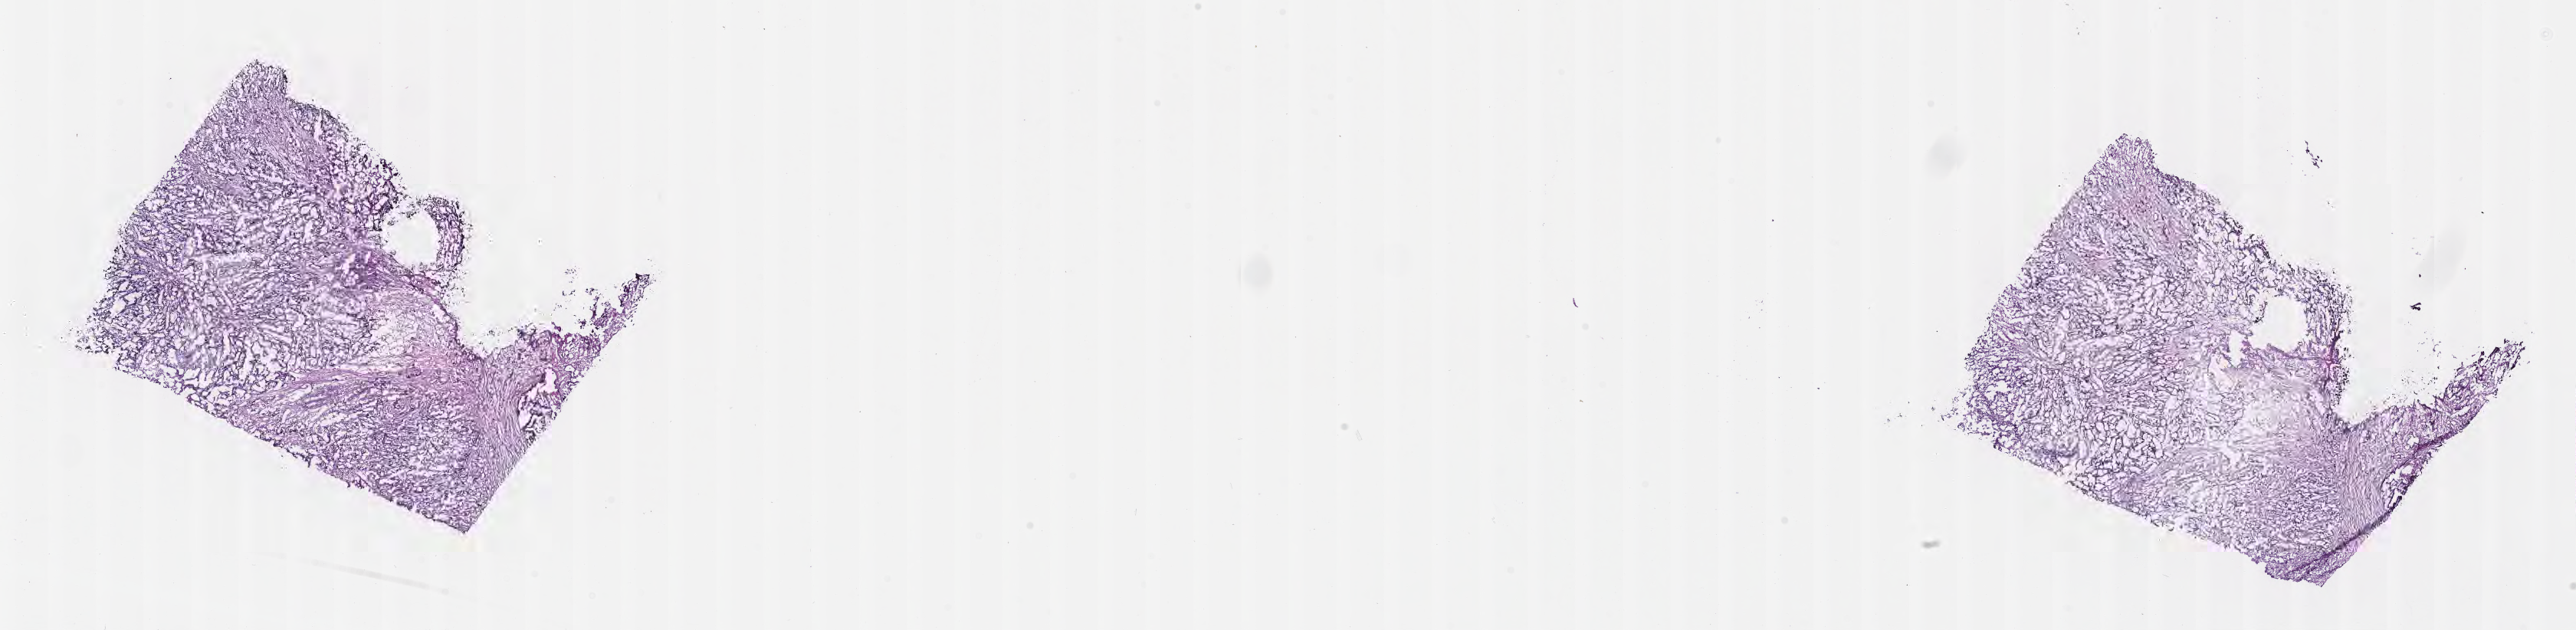
Hematoxylin and eosin (H&E) whole-slide image, shown as a low-resolution overview of the whole scanned area (about 27.2 x 6.6 mm). Frozen section. Metastatic tumor tissue, resected from liver. Female patient; age at initial diagnosis 78 years. Pathologist review of this section (percent, as recorded): tumor cells 50%, tumor nuclei 50%, stromal cells 50%, necrosis 0%, normal cells 0%. Infiltration values recorded for this section: lymphocyte infiltration 0%, monocyte infiltration 0%, neutrophil infiltration 0%.
• patient diagnosis (primary): Adenocarcinoma, NOS
• section: bottom of the tissue portion